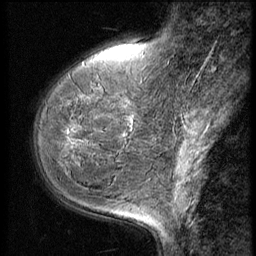
Breast MRI (dynamic contrast-enhanced), one sagittal slice; position 17 of 56 along the scan axis; 3 images stored at this slice position (order not interpretable as contrast timing); 1.5 T; TE 4.2 ms, TR 9 ms; 2.5 mm slice thickness; 256 × 256 image matrix. Patient: female, 49 years. Case-level facts recorded for this patient, not image findings: setting: breast cancer imaged before/during neoadjuvant chemotherapy; receptor status: HER2-positive.
Annotated regions visible in this slice (semi-automatically segmented with operator editing):
- analysis volume of interest (the breast-tissue region the enhancement analysis was run in; not a lesion): bounding box <31,74,148,198> (left, top, right, bottom; pixels)
- tumour enhancement mask (voxels above the 140 % enhancement threshold inside the analysis volume of interest): <72,126,132,141>